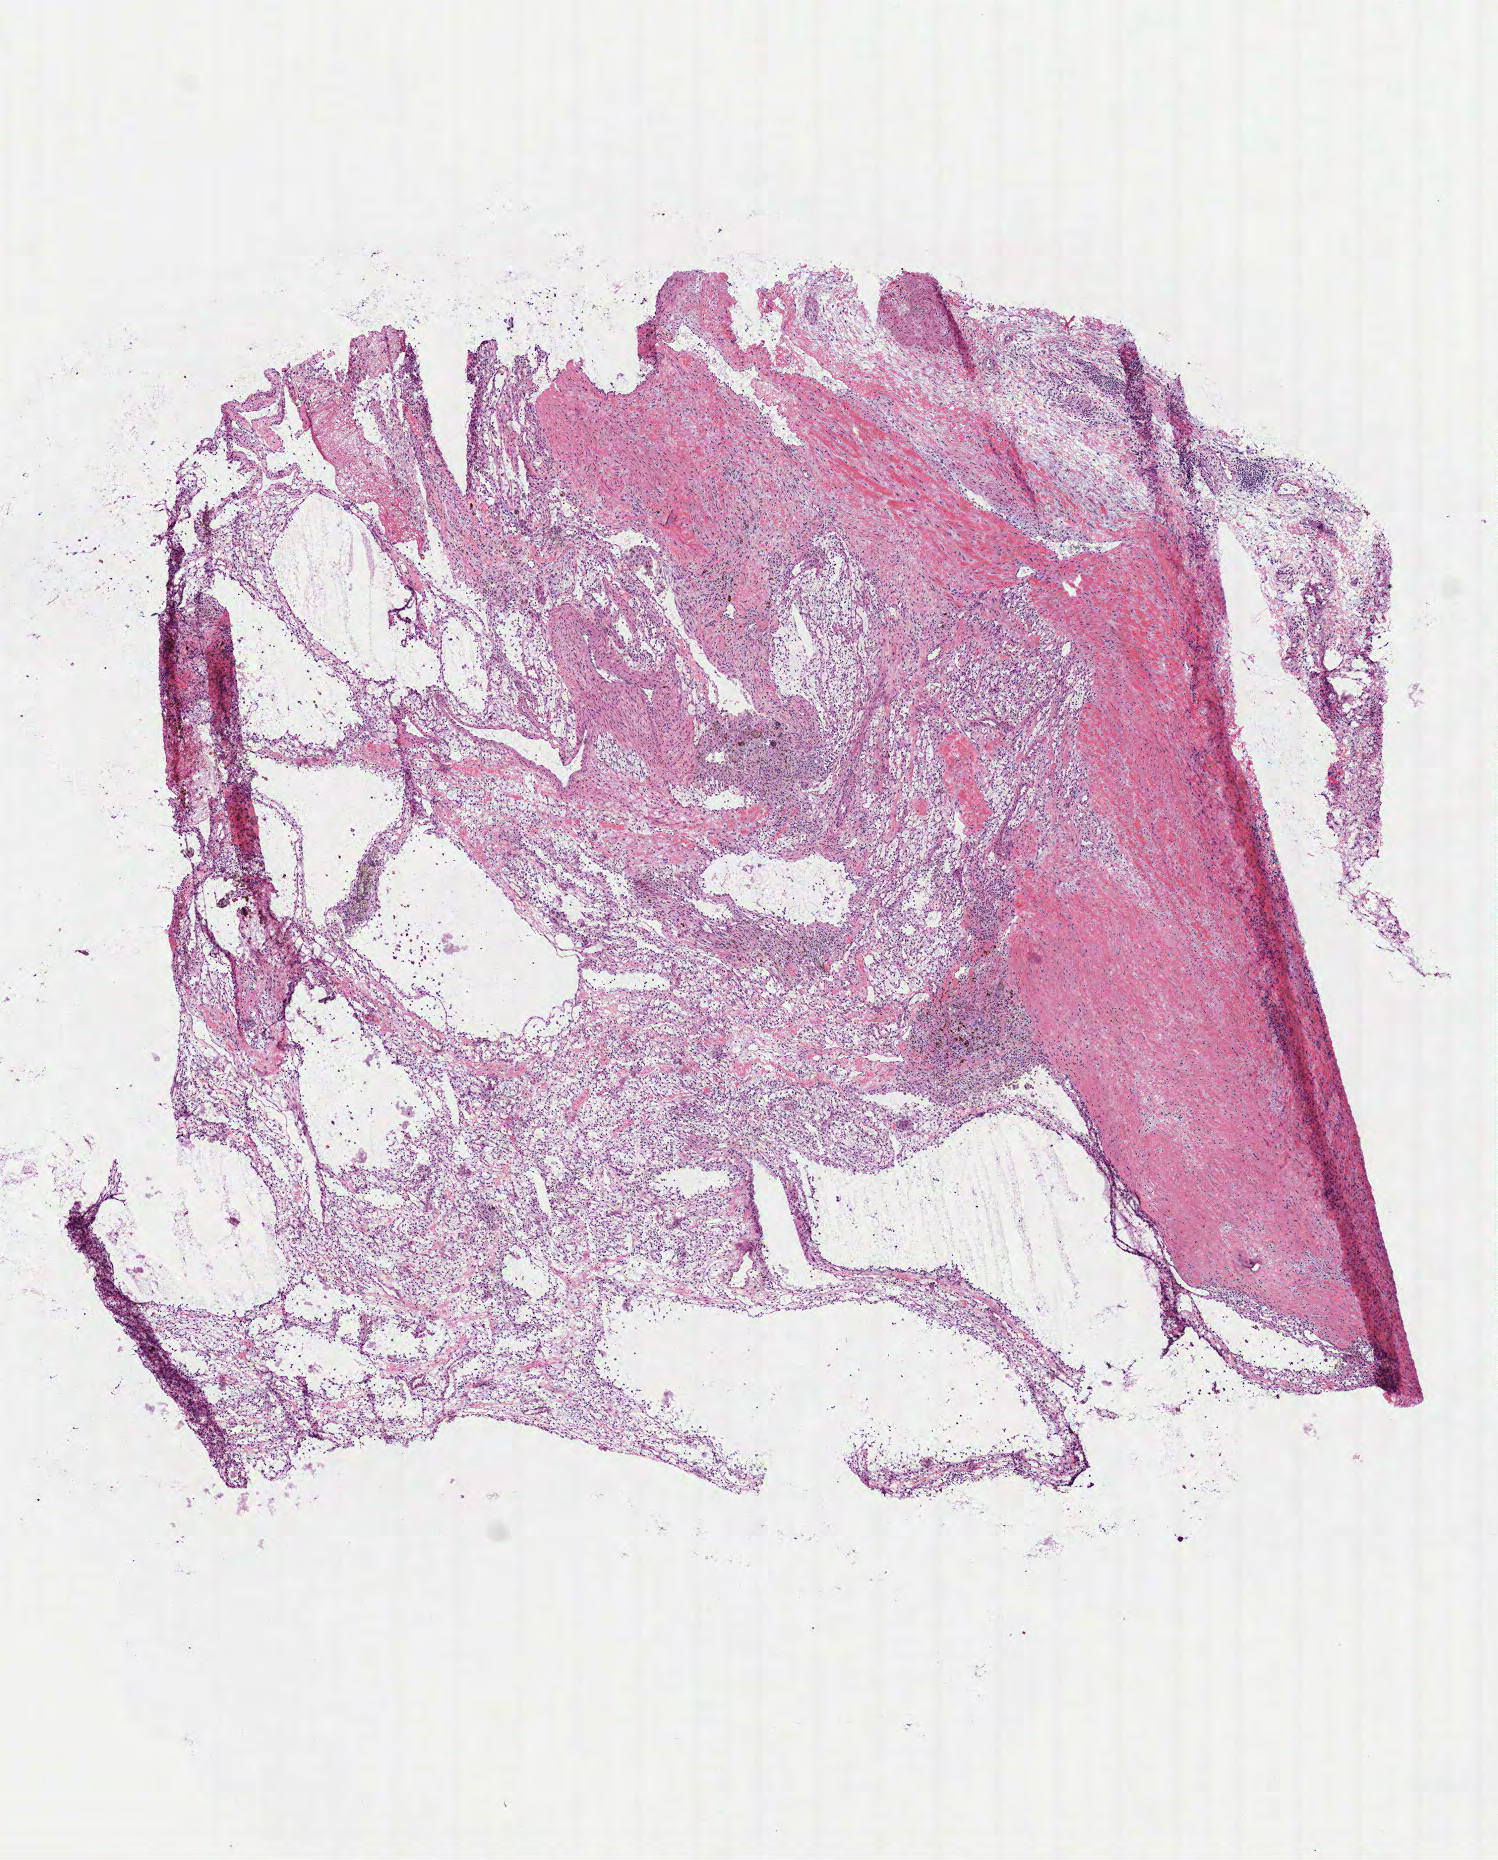
Whole-slide histology image, Hematoxylin and eosin (H&E) stained, low-resolution overview of the scanned area, about 6.0 x 7.5 mm (acquisition: 40x scan). Frozen section from the top of the tissue portion. Sample: primary tumour, kidney. Patient: female, age at initial diagnosis 41 years. Histologic grade: G2 (moderately differentiated). Pathologist review of this section (percent, as recorded): tumour cells 75%, tumour nuclei 80%, normal cells 0%, stromal cells 25%, necrosis 0%.
* laterality: right
* pathologic diagnosis: Clear cell adenocarcinoma, NOS
* AJCC pathologic stage: I